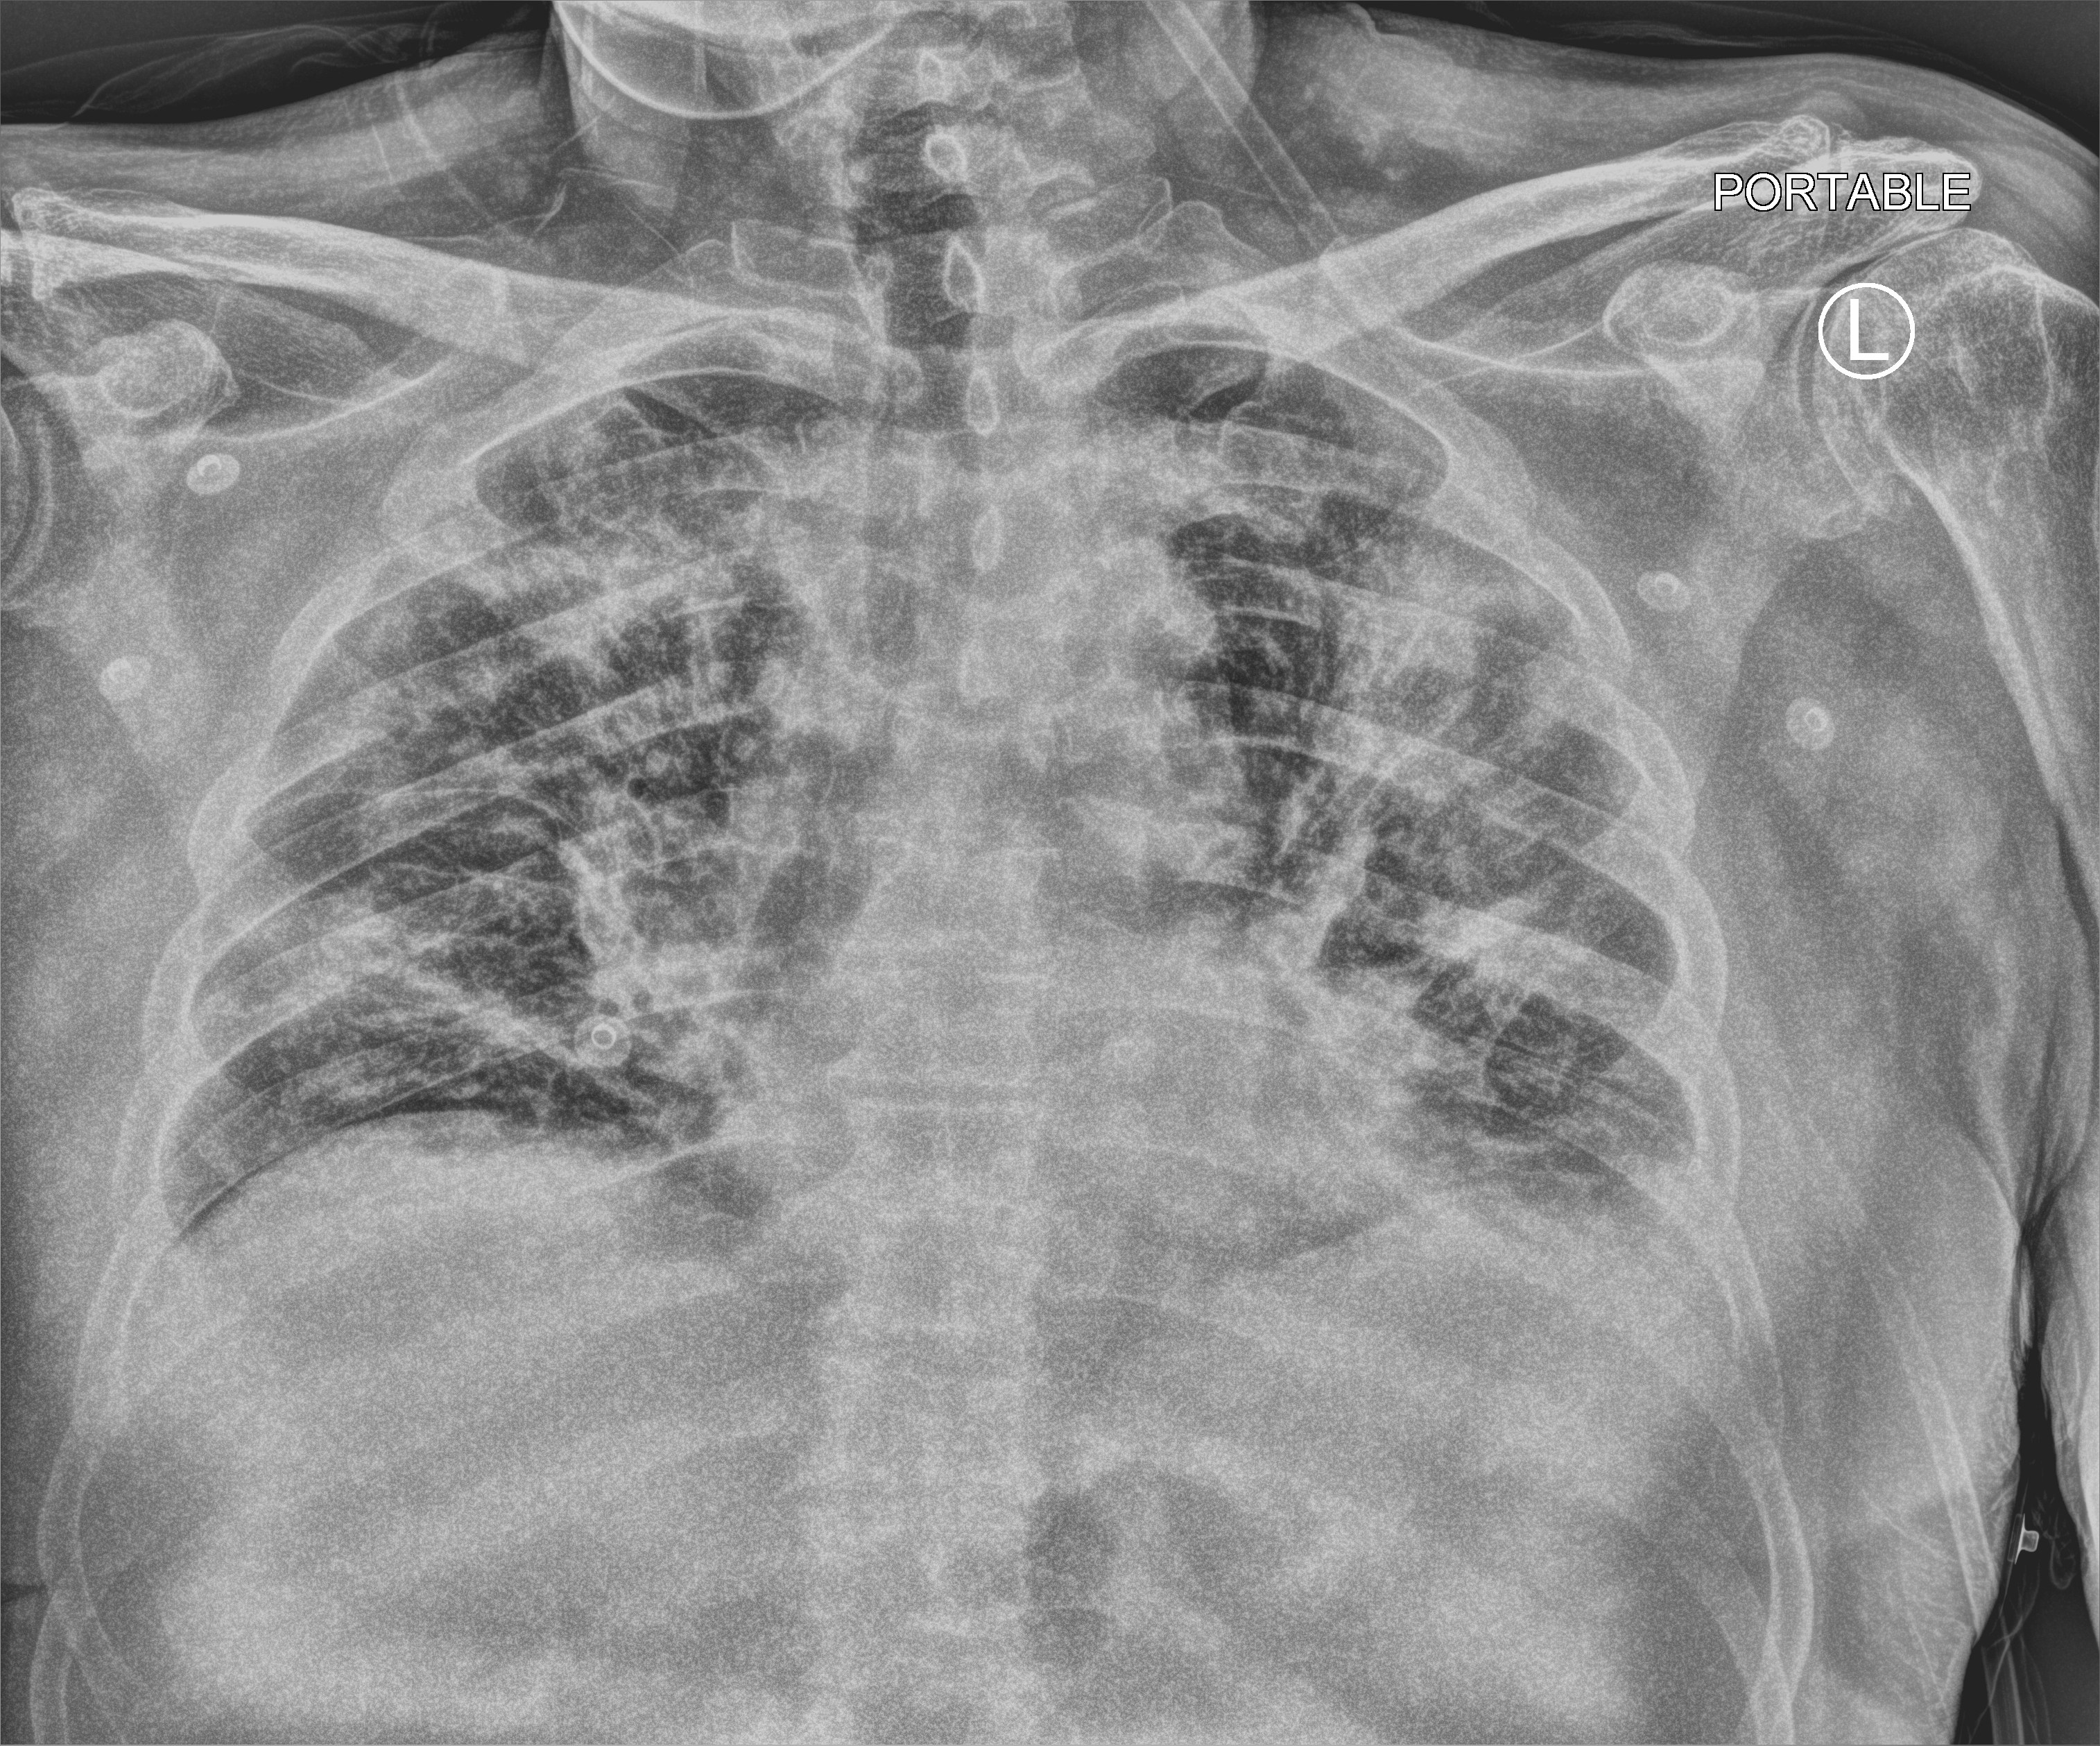
Portable chest radiograph, anteroposterior (AP) projection. Male patient hospitalised with COVID-19, age 60–74 years.
Admission-level facts for this patient (not findings on this image; timing relative to this image not recorded): mechanically ventilated during this hospital stay: no; length of hospital stay: 20 days.